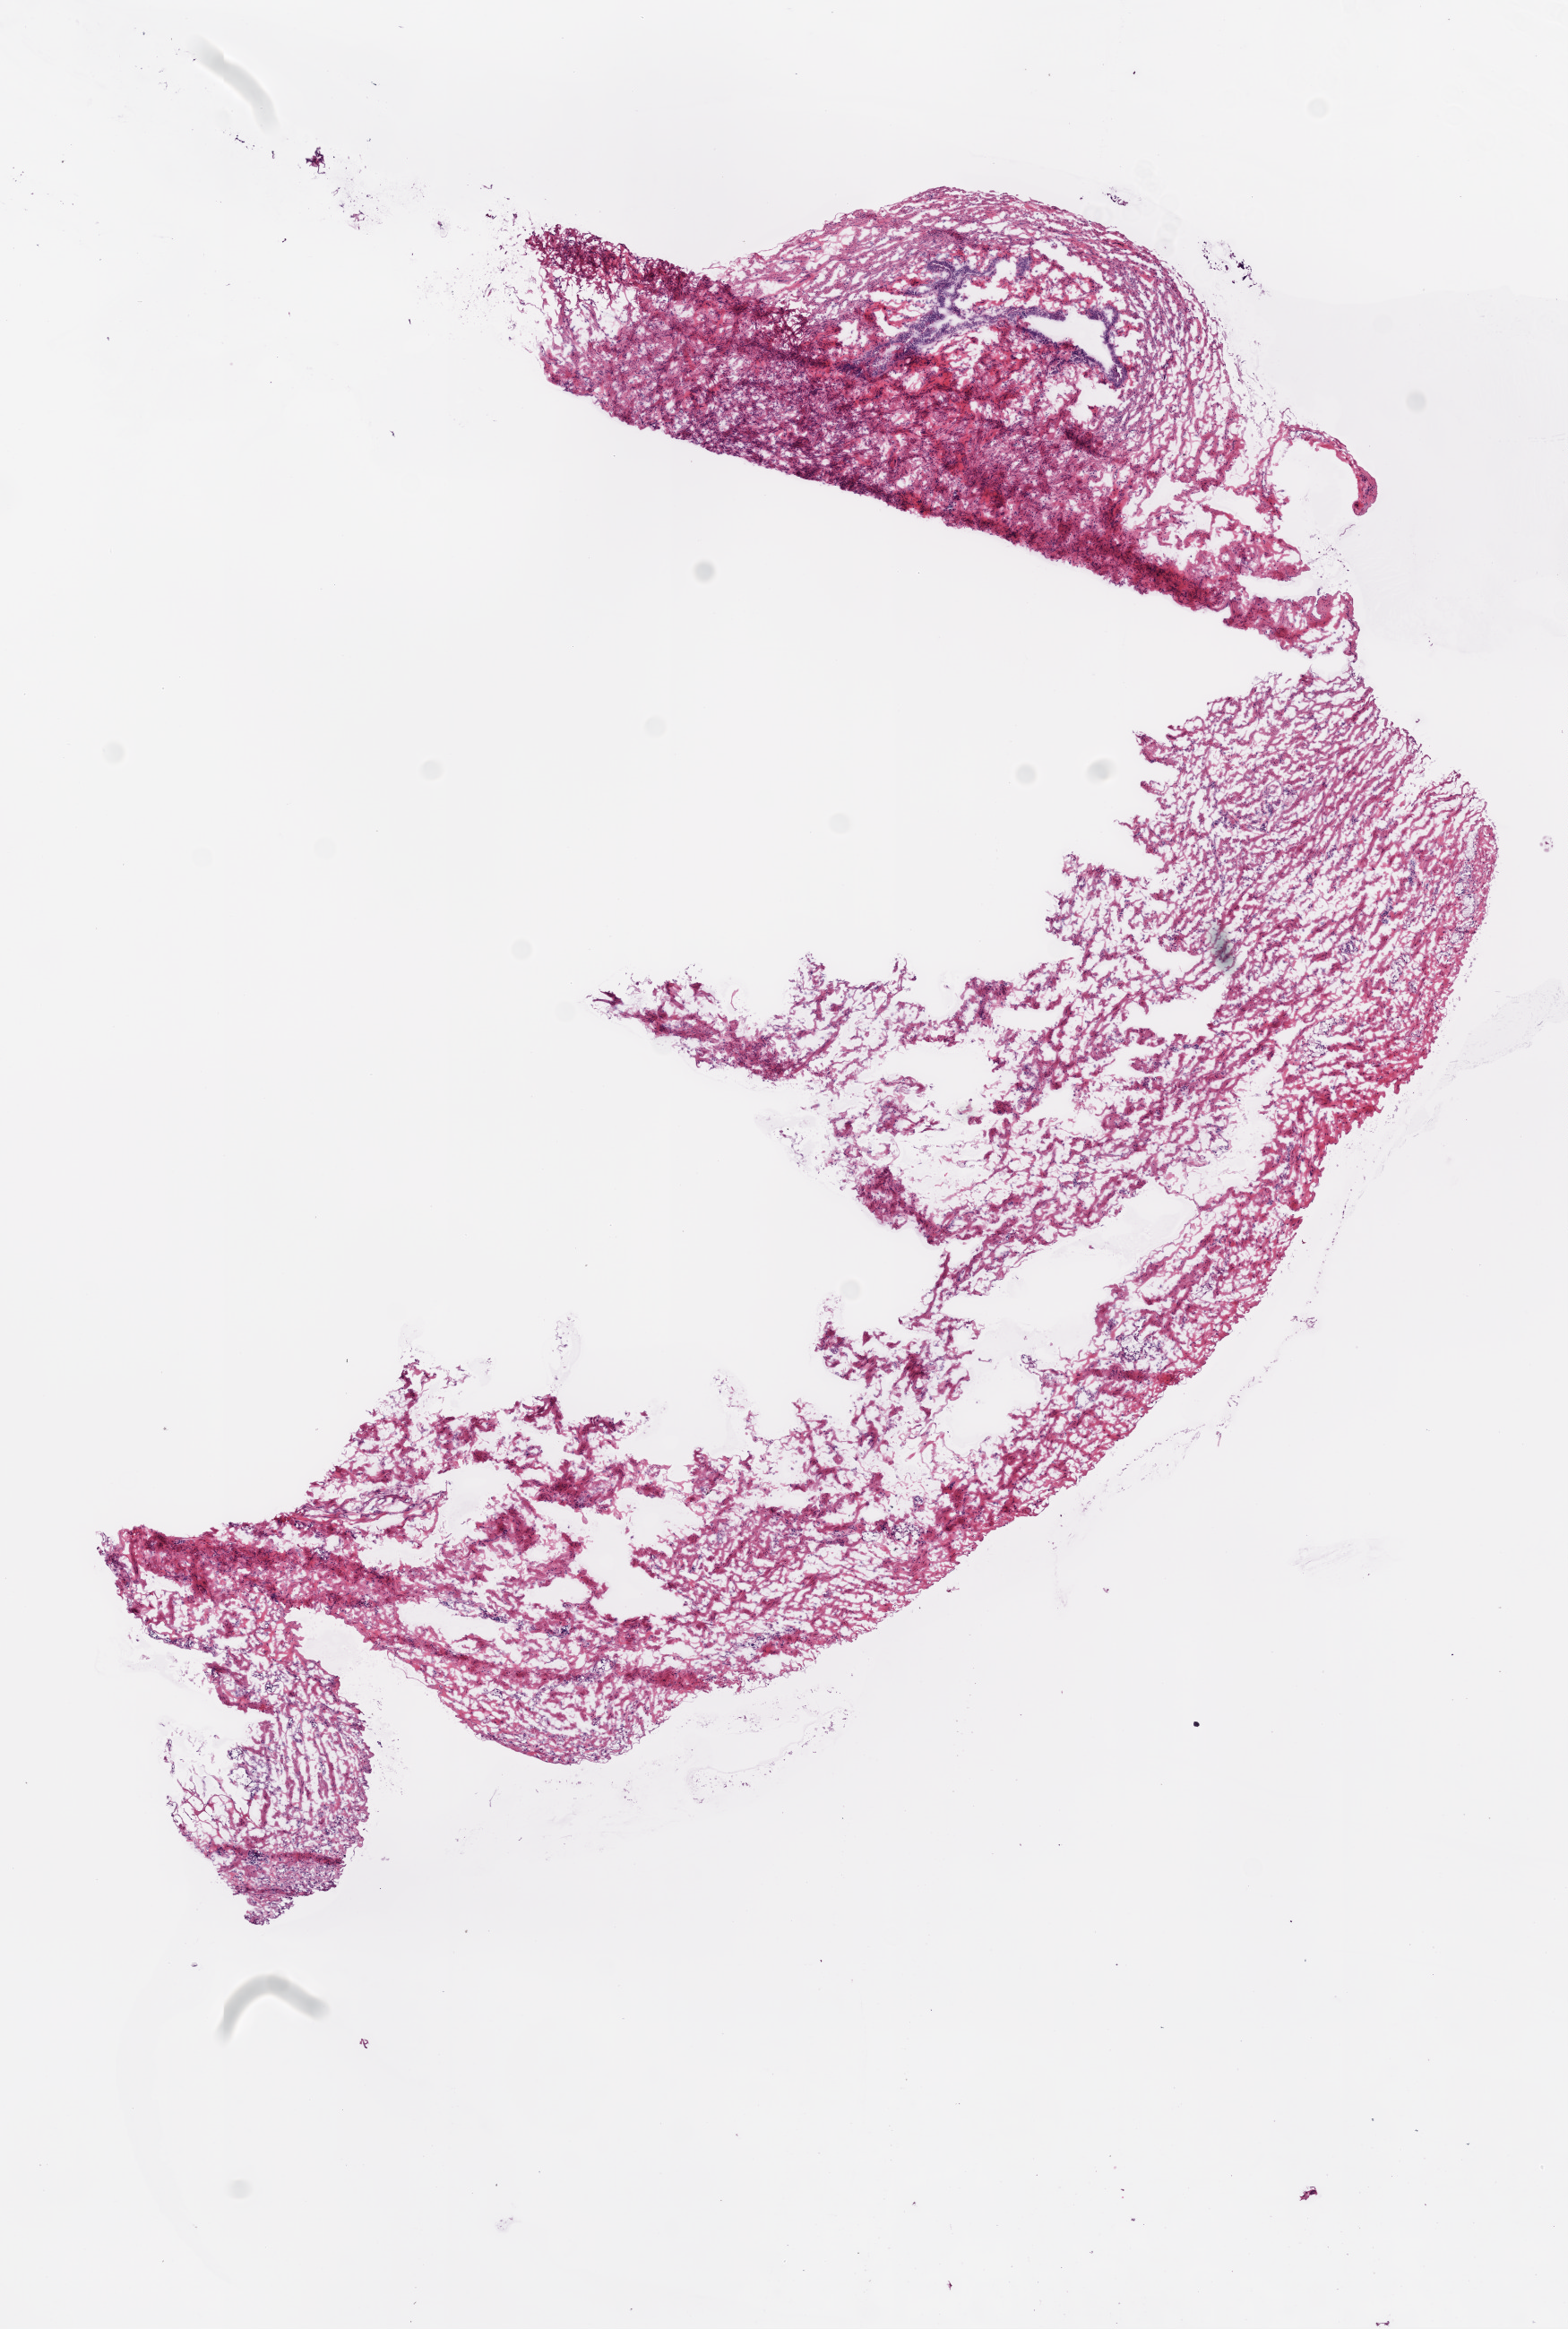
H&E-stained whole-slide image, a low-resolution overview of the entire scanned area, about 7.0 x 10.4 mm (slide scanned at 20x), frozen section from the bottom of the tissue portion, solid tissue normal (non-tumour tissue) sample from the ovary. Female patient; age at initial diagnosis 56 years.
This section: solid tissue normal sample (biorepository sample class). Patient diagnosis: Serous cystadenocarcinoma, NOS.